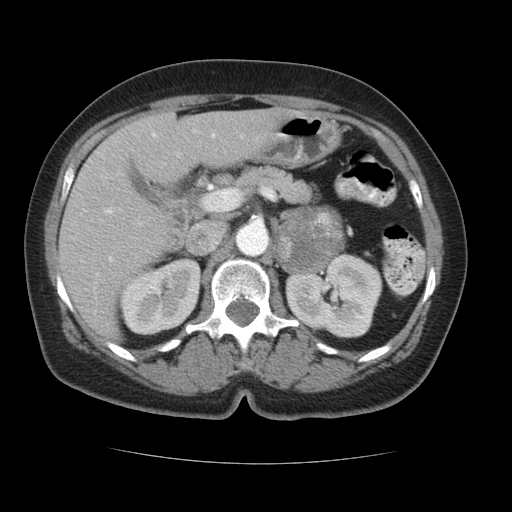
Contrast-enhanced abdominal CT, one axial slice; reconstruction kernel STANDARD; intravenous contrast given; soft-tissue window (W 400 / L 40 HU); 5 mm slice thickness; 512 × 512 image matrix, field of view 348 × 348 mm. Patient: female, 66 years. Case-level facts recorded for this patient, not image findings: diagnosis: adrenocortical carcinoma; tumour side: left adrenal; tumour size at pathology: 5.5 cm; Ki-67 index: 15 %; stage (as recorded): 3.
Structures marked on this image (semi-automatic segmentation, software-assisted and operator-edited):
- mass: bounding box <280,211,341,271> (left, top, right, bottom; pixels)